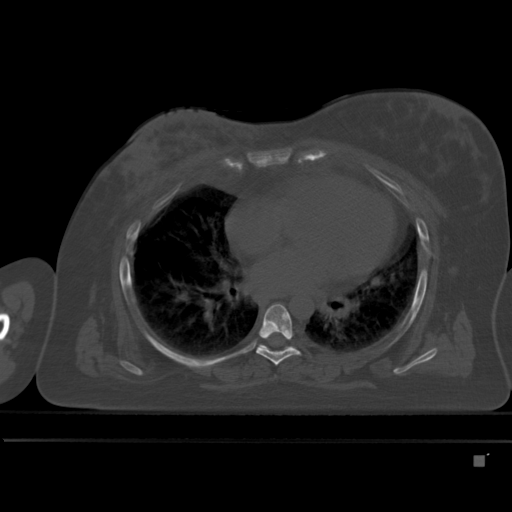
CT including the spine, one axial slice; slice 304 of 495 in the series (ordered by position); bone window (W 1800 / L 400 HU); 1.5 mm slice thickness; 512 × 512 image matrix. Female patient, age 33 years. Case-level facts recorded for this patient, not image findings: primary cancer: breast.
Annotated regions visible in this slice (semi-automatically segmented with operator editing):
- T6 vertebra: box from (x=255, y=304) to (x=301, y=366) px
- T7 vertebra: (x=257, y=345)–(x=294, y=349)